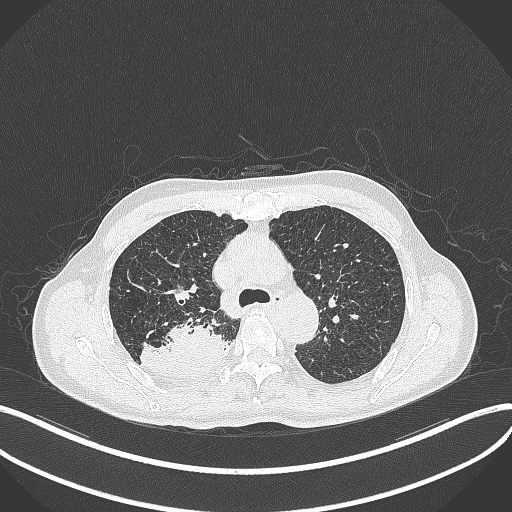
Chest CT, one axial slice. Position 316 of 428 along the scan axis. 120 kVp. Lung window (W 1500 / L -600 HU). 512 × 512 image matrix. Male patient, age 79 years. Case-level facts recorded for this patient, not image findings: clinical TNM (as recorded): T3 N0 M0.
Annotated regions visible in this slice (bounding box drawn by a radiologist):
- lung tumour (recorded histology: adenocarcinoma): box from (x=138, y=317) to (x=226, y=377) px